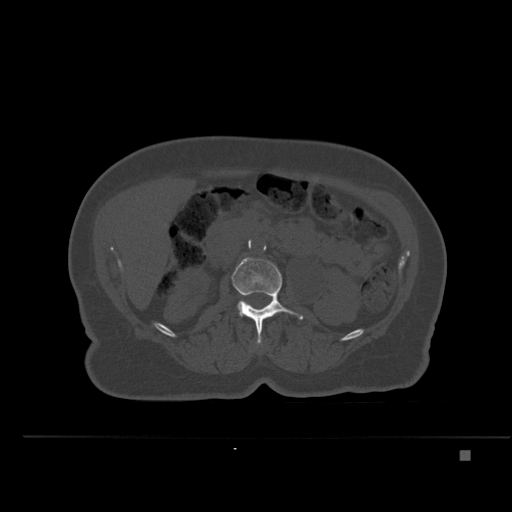
CT including the spine, one axial slice; slice 215 of 477 in the series (ordered by position); bone window (W 1800 / L 400 HU); 1.5 mm slice thickness; 512 × 512 image matrix, field of view 422 × 422 mm. Patient: female, 74 years. From the clinical record (not read from this slice): primary cancer: colon.
Annotated regions visible in this slice (semi-automatic segmentation, software-assisted and operator-edited):
- L2 vertebra: bounding box <232,257,304,344> (left, top, right, bottom; pixels)